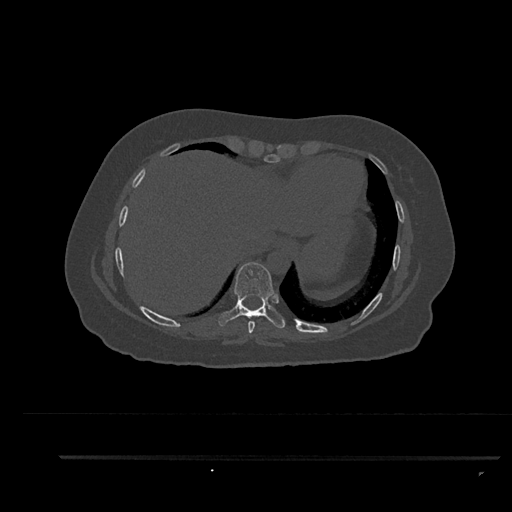
CT including the spine, one axial slice; slice 422 of 797 in the series (ordered by position); reconstruction kernel Br40s/3; bone window (W 1800 / L 400 HU); 0.5 mm slice thickness; 512 × 512 image matrix. Patient: female, 44 years. From the clinical record (not read from this slice): primary cancer: renal; vertebrae with lytic lesions (as recorded): L1.
Annotated regions visible in this slice (semi-automatically segmented with operator editing):
- T8 vertebra: box from (x=248, y=321) to (x=255, y=333) px
- T9 vertebra: (x=218, y=262)–(x=285, y=328)